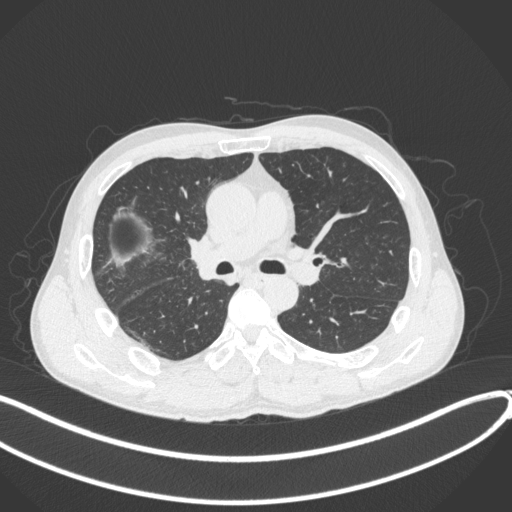
Chest CT, one axial slice; slice 230 of 409 in the series (ordered by position); reconstruction kernel B31f; 120 kVp; lung window (W 1500 / L -600 HU); 512 × 512 image matrix, field of view 400 × 400 mm. Patient: male, 53 years. Case-level facts recorded for this patient, not image findings: clinical TNM (as recorded): T1b N0 M0.
Outlined on this slice (rectangle marked by the reading radiologist):
- lung tumour (recorded histology: squamous cell carcinoma): bounding box [x1, y1, x2, y2] px = [185, 230, 224, 289]